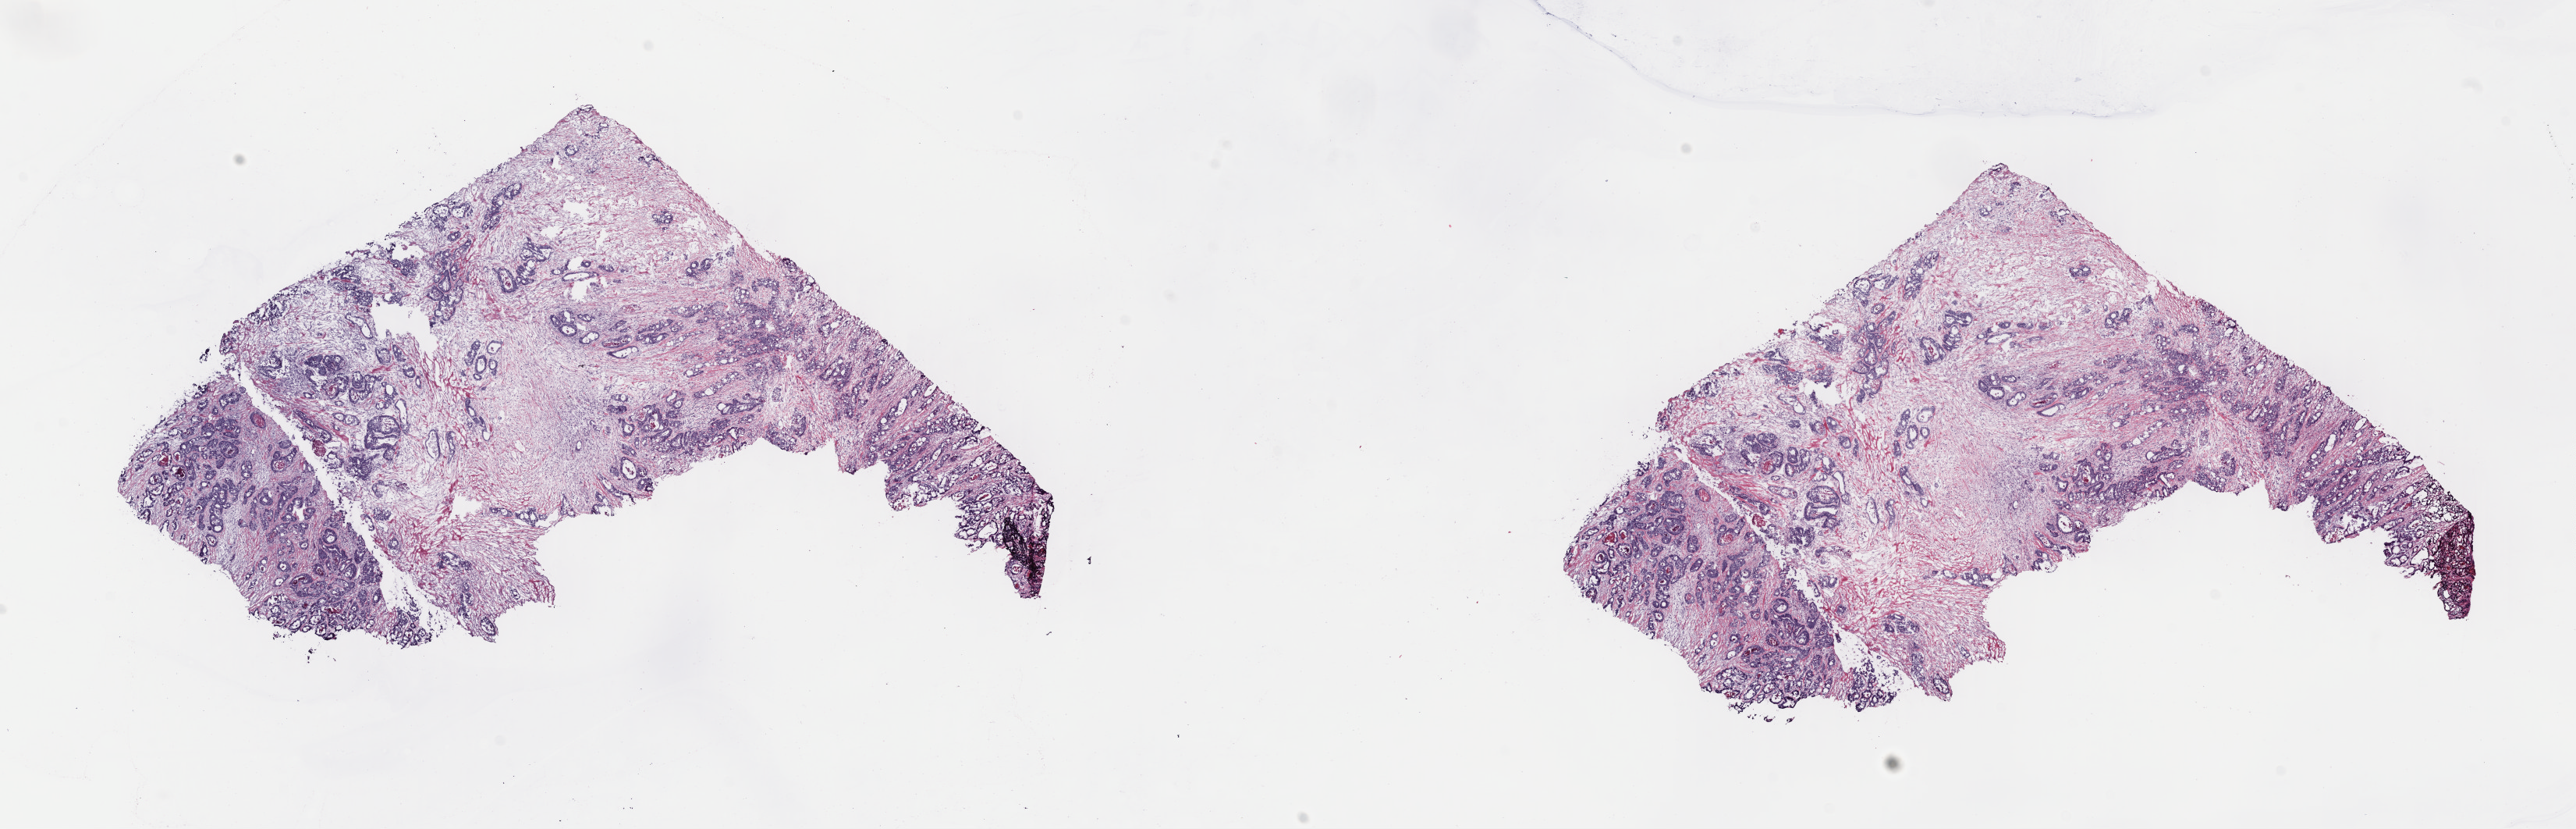
Digitized Hematoxylin and eosin (H&E) stained tissue section (whole slide), shown as a low-resolution overview of the whole scanned area (about 26.0 x 8.3 mm, slide scanned at 40x), frozen section from the top of the tissue portion, primary tumour sample from the colon. Male, age 42 years at initial diagnosis. Composition of this section per pathologist review: tumour cells 95%, tumour nuclei 60%.
Diagnosis: Mucinous adenocarcinoma (cecum).